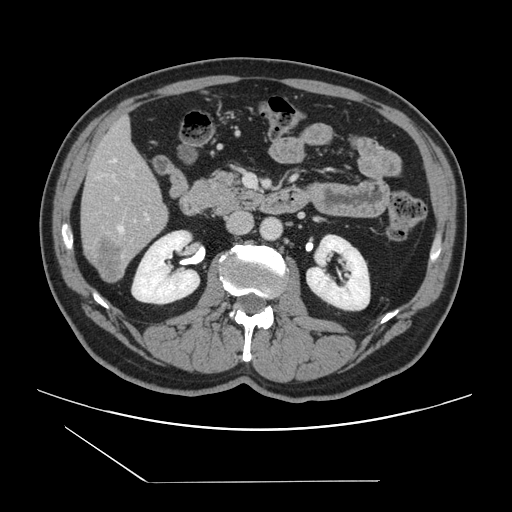
Contrast-enhanced abdominal CT, one axial slice; position 53 of 157 along the scan axis; 120 kVp; intravenous contrast given; soft-tissue window (W 400 / L 40 HU); 2.5 mm slice thickness; 512 × 512 image matrix. Male patient, age 61 years. Case-level facts recorded for this patient, not image findings: diagnosis: colorectal cancer liver metastases, imaged before liver resection; multiple liver metastases: yes; largest metastasis: 5.5 cm; disease in both lobes: yes.
Structures marked on this image (manually delineated by an expert):
- hepatic veins: bounding box [x1, y1, x2, y2] px = [113, 159, 124, 232]
- liver: [82, 120, 168, 281]
- planned liver remnant (the part of the liver to remain after resection): [82, 120, 164, 218]
- portal vein (with intrahepatic branches): [116, 197, 150, 220]
- liver metastasis: [92, 239, 125, 280]